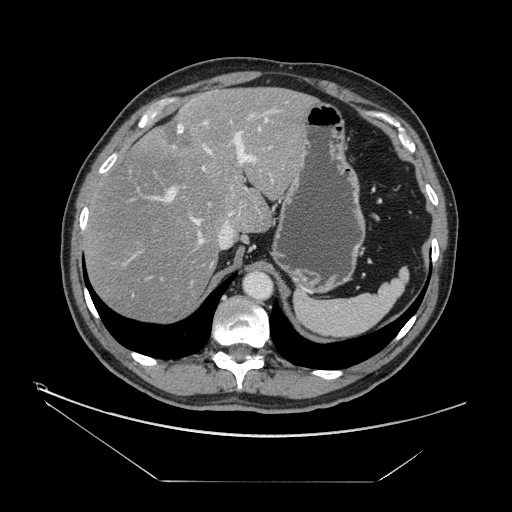
Contrast-enhanced abdominal CT, one axial slice. 120 kVp. Intravenous contrast given. Soft-tissue window (W 400 / L 40 HU). 2.5 mm slice thickness. 512 × 512 image matrix, field of view 440 × 440 mm. Male patient, age 65 years. From the clinical record (not read from this slice): diagnosis: colorectal cancer liver metastases, imaged before liver resection.
Outlined on this slice (manually delineated by an expert):
- hepatic veins: box from (x=193, y=119) to (x=267, y=265) px
- liver: (x=85, y=88)–(x=313, y=323)
- planned liver remnant (the part of the liver to remain after resection): (x=85, y=88)–(x=312, y=323)
- portal vein (with intrahepatic branches): (x=150, y=101)–(x=289, y=224)
- liver metastasis: (x=166, y=122)–(x=195, y=152)